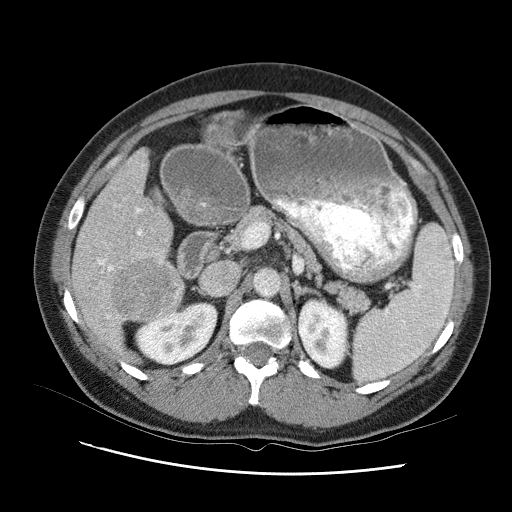
Contrast-enhanced abdominal CT (liver protocol), one axial slice. Position 47 of 95 along the scan axis. Reconstruction kernel STANDARD. One of 2 acquisitions stored at this slice position. Soft-tissue window (W 400 / L 40 HU). 2.5 mm slice thickness. 512 × 512 image matrix, field of view 360 × 360 mm. Case-level facts recorded for this patient, not image findings: diagnosis: hepatocellular carcinoma (patient treated with transarterial chemoembolisation; whether this scan precedes or follows treatment is not stated here); TNM stage (as recorded): Stage-I; Child-Pugh class: B.
Outlined on this slice (semi-automatic segmentation, software-assisted and operator-edited):
- liver parenchyma outside the tumour (the mass and vessels are separate outlines, so this box may not span the whole liver): box from (x=68, y=136) to (x=186, y=366) px
- mass: (x=117, y=249)–(x=188, y=315)
- liver vessels: (x=105, y=166)–(x=183, y=331)